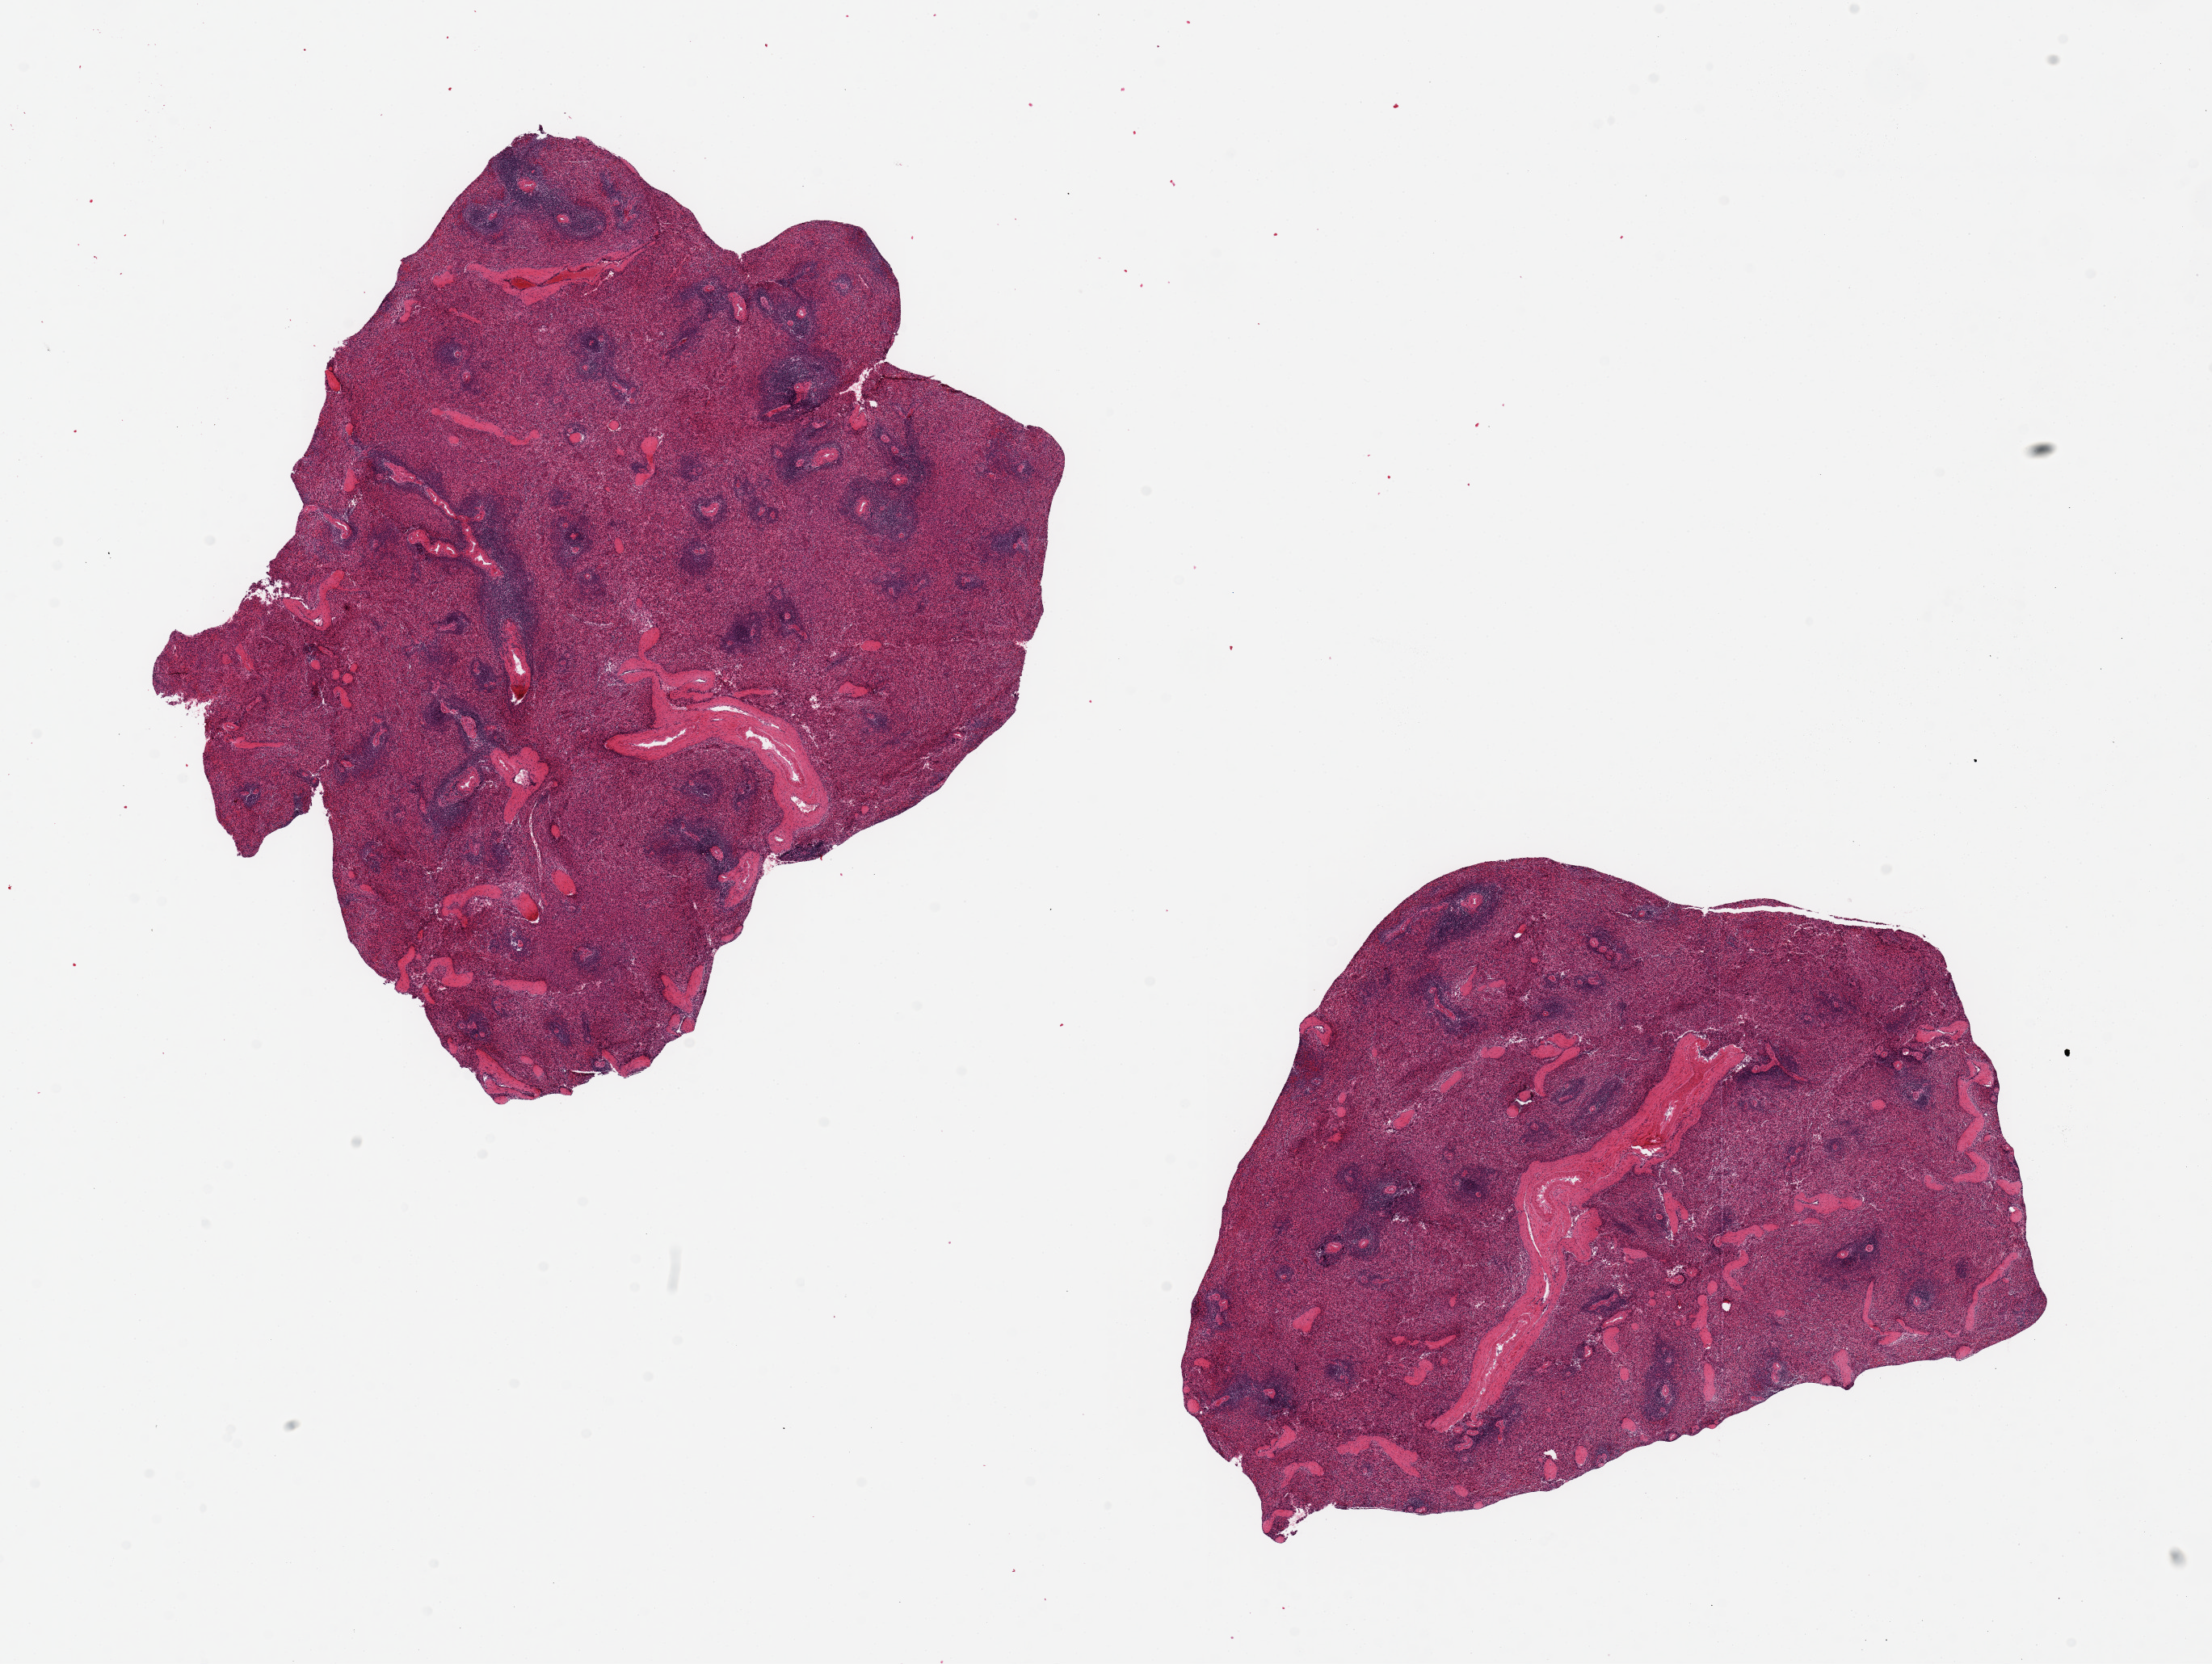
Whole-slide image, H&E stain, brightfield, low-resolution overview of the scanned area, about 21.7 x 16.3 mm (from a 20x scan), PAXgene-fixed paraffin-embedded (PFPE) section, sampled site (target tissue): spleen, donor tissue sample. Donor sex: male.
Review note (as recorded): 2 pieces ~7x7mm, moderate congestion.